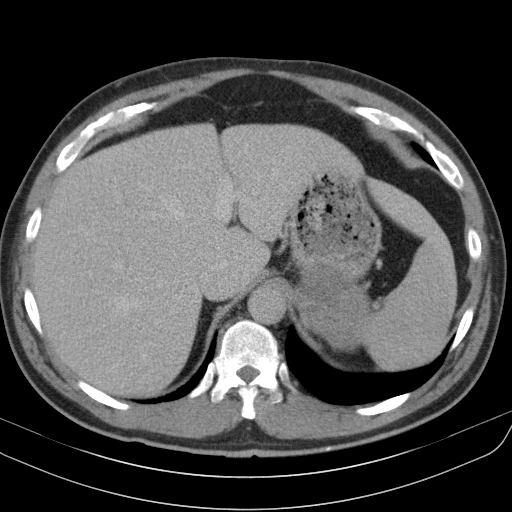
Contrast-enhanced abdominal CT, one axial slice. Slice 79 of 91 in the series (ordered by position). 130 kVp. Intravenous contrast given. Soft-tissue window (W 400 / L 40 HU). 5 mm slice thickness. 512 × 512 image matrix, field of view 370 × 370 mm. Male patient, age 51 years. From the clinical record (not read from this slice): diagnosis: adrenocortical carcinoma; tumour side: left adrenal; tumour size at pathology: 18 cm; Ki-67 index: 40 %; stage (as recorded): 3.
Annotated regions visible in this slice (semi-automatic segmentation, software-assisted and operator-edited):
- mass: box from (x=298, y=265) to (x=369, y=350) px